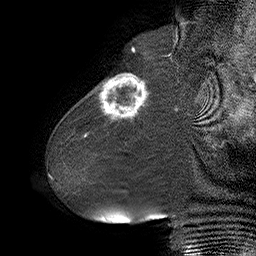
Breast MRI (dynamic contrast-enhanced), one sagittal slice. Position 15 of 55 along the scan axis. Dynamic contrast-enhanced series, time point 2 of 6 at this slice position (early post-contrast). 1.5 T. TE 4.5 ms, TR 32.4 ms. 3 mm slice thickness. 256 × 256 image matrix, field of view 180 × 180 mm. Female patient. Case-level facts recorded for this patient, not image findings: setting: breast cancer imaged before/during neoadjuvant chemotherapy; receptor status: HER2-positive.
Structures marked on this image (semi-automatically segmented with operator editing):
- analysis volume of interest (the breast-tissue region the enhancement analysis was run in; not a lesion): box from (x=80, y=64) to (x=163, y=134) px
- tumour enhancement mask (voxels above the 100 % enhancement threshold inside the analysis volume of interest): (x=98, y=74)–(x=148, y=121)